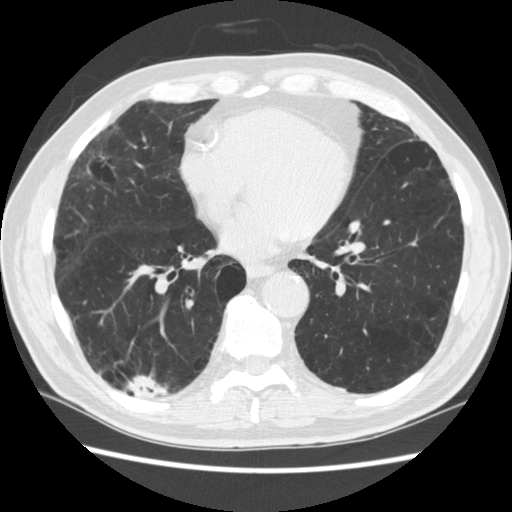
Chest CT (low-dose screening protocol), one axial image, third screening round (two years after baseline), lung window (W 1500 / L -600 HU), standard (soft-tissue) reconstruction kernel (STANDARD), 120 kVp, slice 155 of 266 in the series, 512 × 512 image matrix, field of view 360 × 360 mm. Male participant, aged 70 years at enrolment. Former smoker at enrolment.
Expert-annotated lung lesion, bounding box <127,360,180,416> (left, top, right, bottom; pixels). The screening reader recorded 4 non-calcified nodules or masses ≥4 mm on this exam; which of them this box marks is not recorded. Later outcome: lung cancer diagnosed 253 days after this screen — squamous cell carcinoma, NOS, right upper lobe, poorly differentiated (G3), stage IV (AJCC 6th edition).